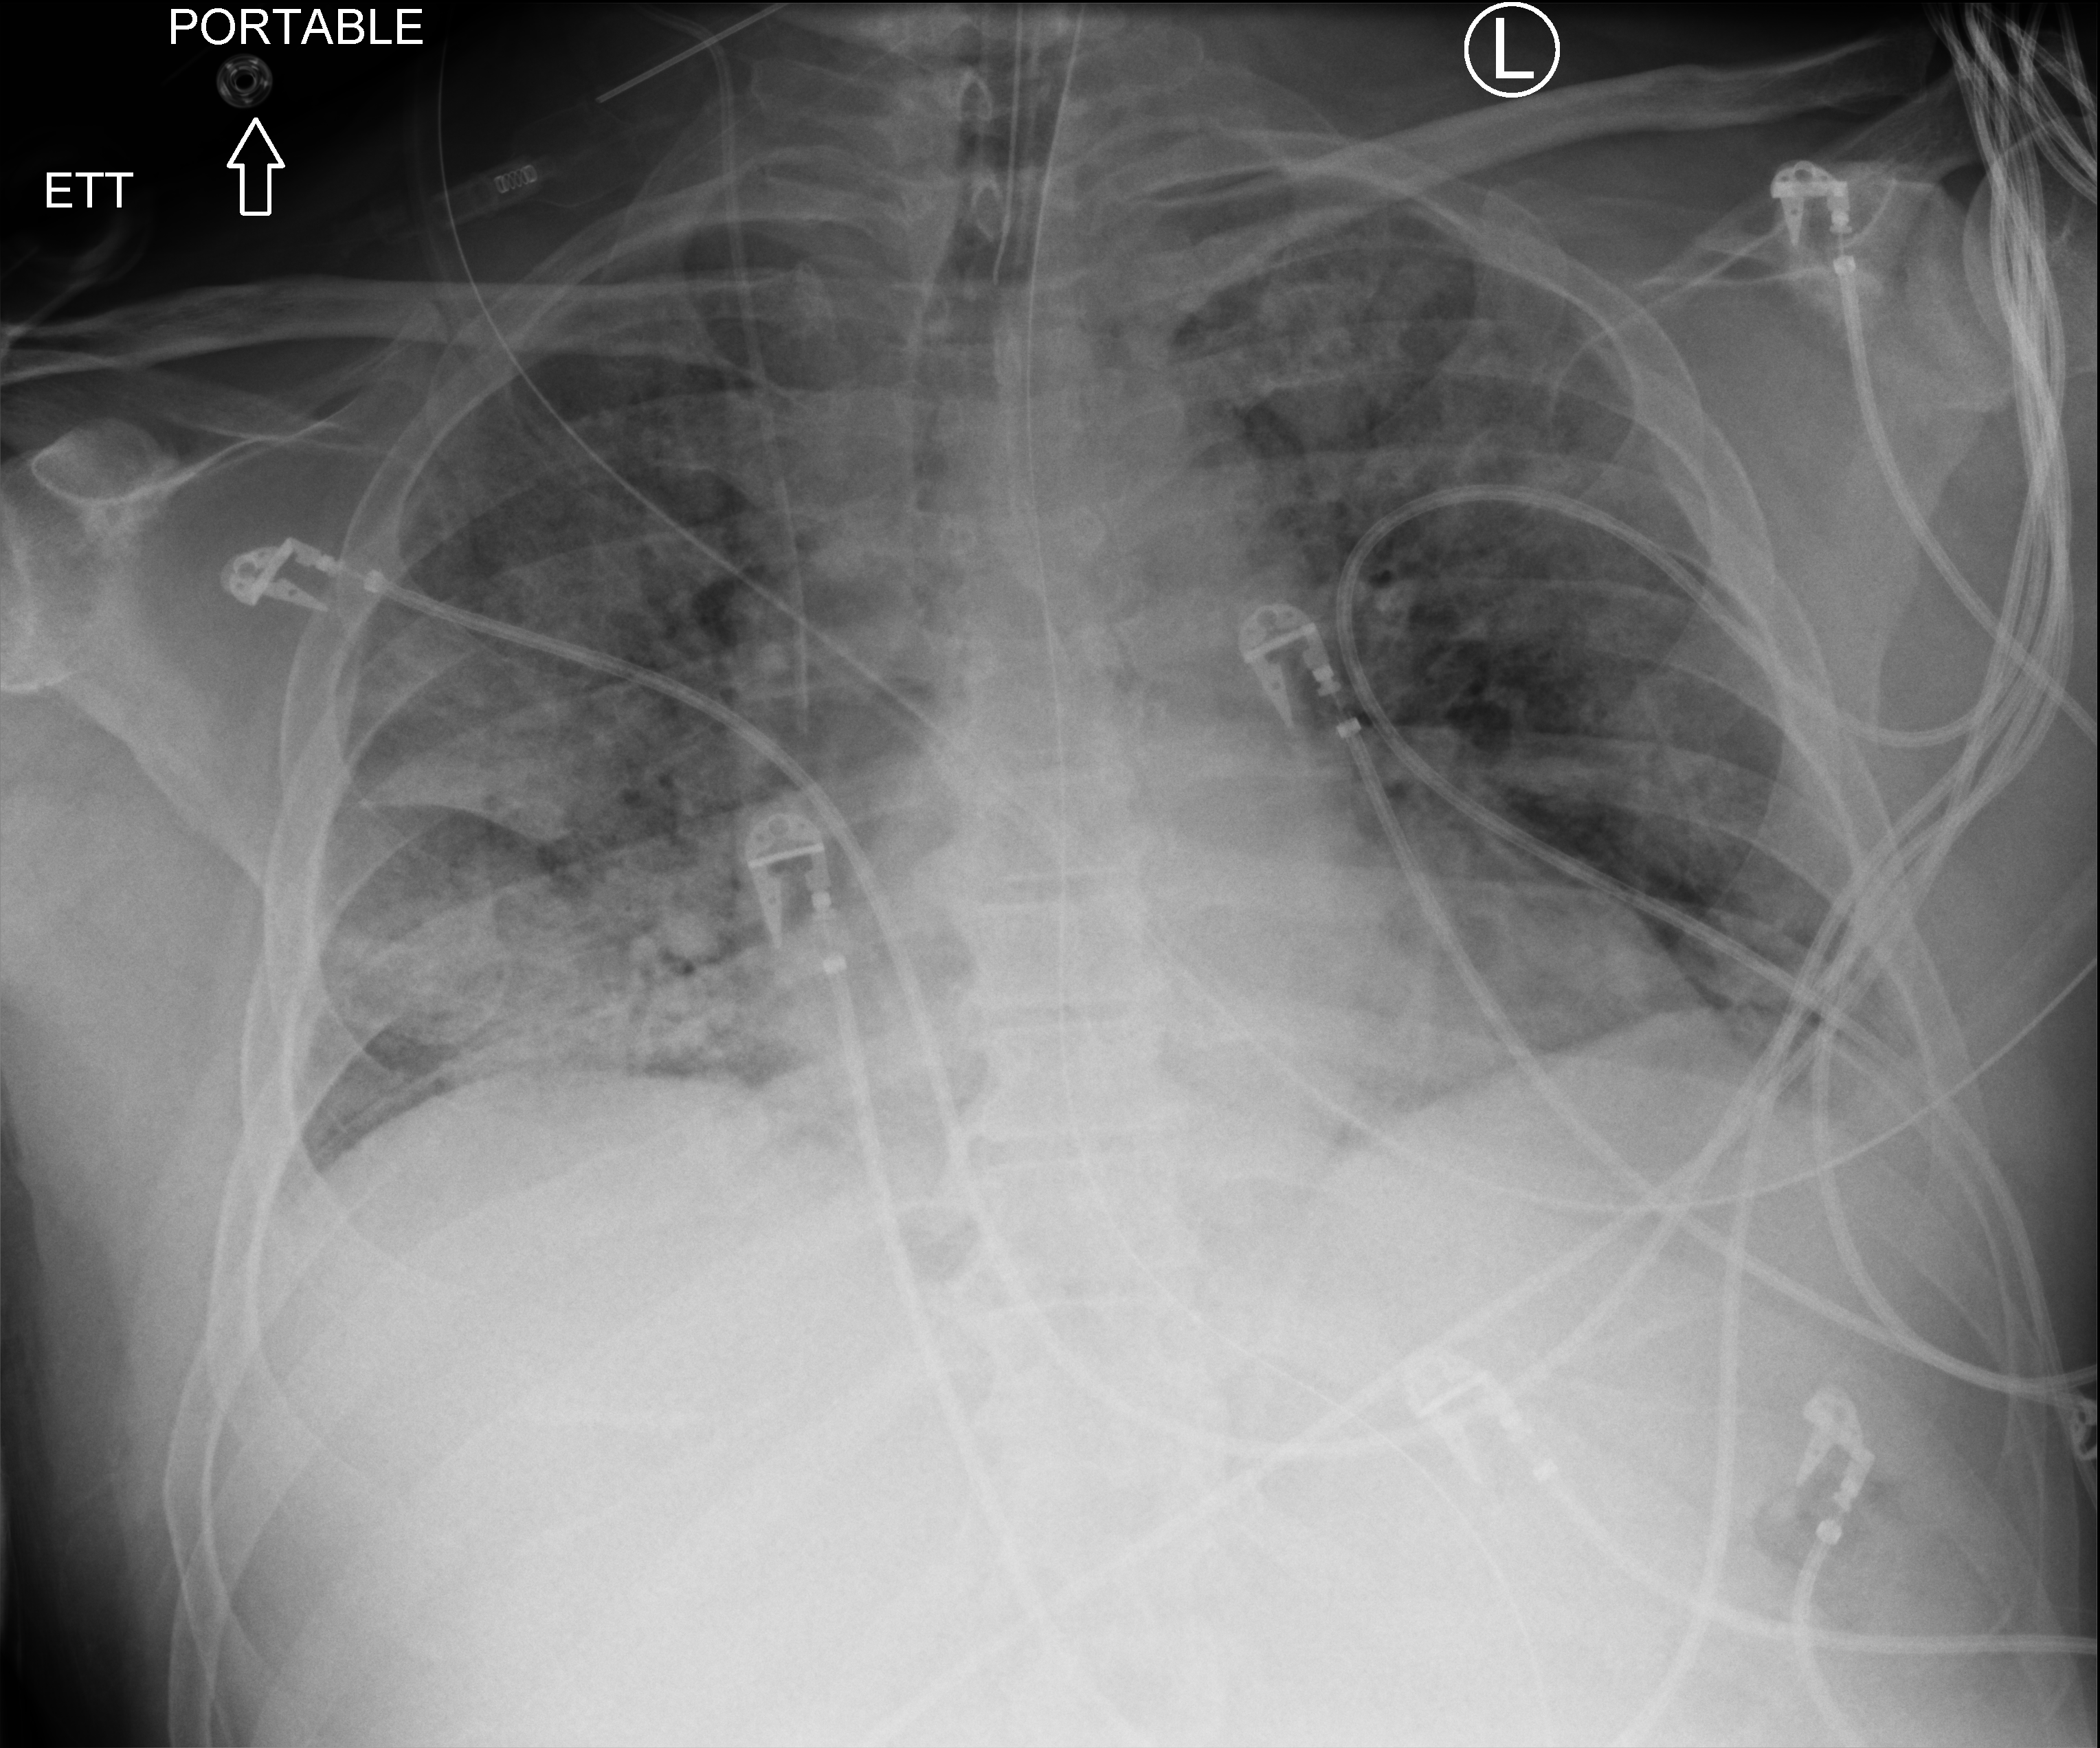
Portable chest radiograph, anteroposterior (AP) projection. Patient hospitalised with COVID-19; male, aged 60–74 years.
Hospital-stay facts (about this admission, not read from this image; timing relative to this image not recorded):
- admitted to intensive care during this hospital stay: yes
- length of hospital stay: 33 days
- mechanically ventilated during this hospital stay: yes